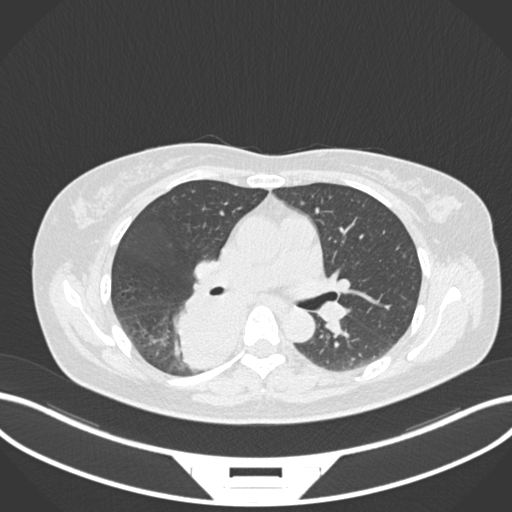
Chest CT, one axial slice. 120 kVp. Lung window (W 1500 / L -600 HU). 1 mm slice thickness. 512 × 512 image matrix. Patient: female, 54 years. Case-level facts recorded for this patient, not image findings: clinical TNM (as recorded): T4 N0 M0.
Annotated regions visible in this slice (bounding box drawn by a radiologist):
- lung tumour (recorded histology: adenocarcinoma): bounding box (x1, y1, x2, y2) in pixels: (170, 287, 243, 371)